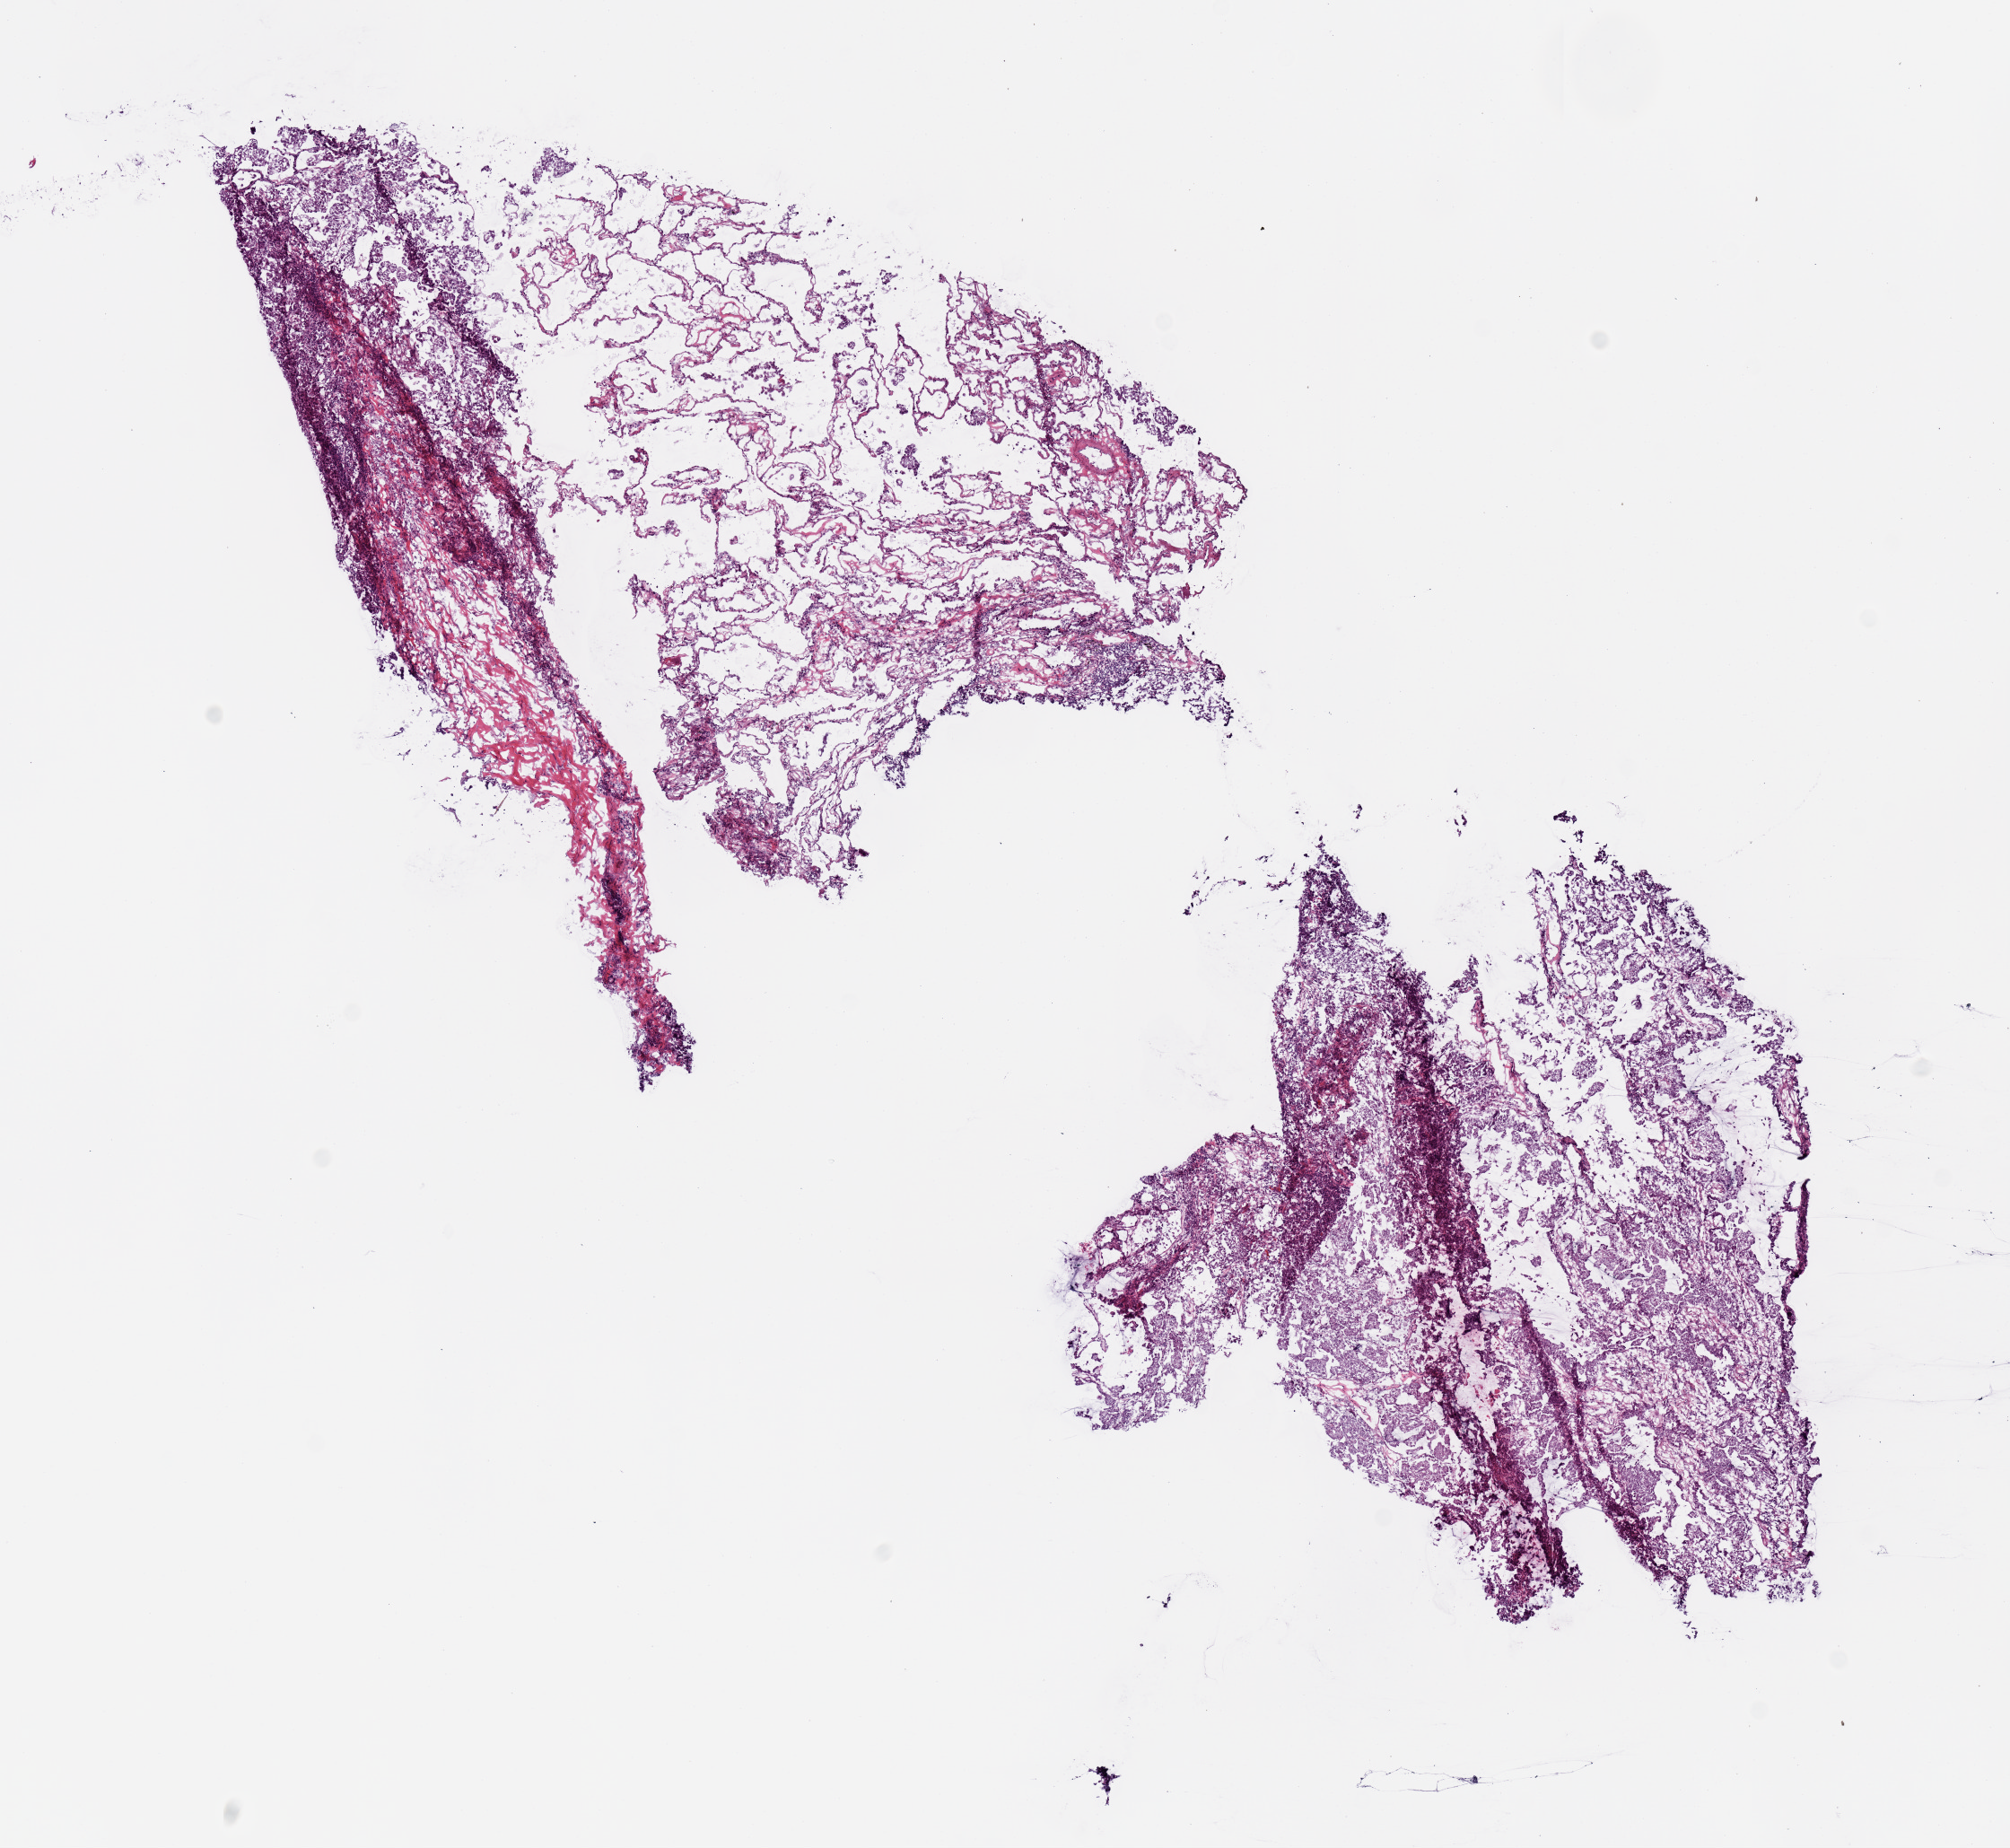
Whole-slide histology image, H&E-stained — shown as a low-resolution overview of the whole scanned area (about 8.9 x 8.1 mm, from a 20x scan). Frozen section from the bottom of the tissue portion. Primary tumour sample from the lung. Patient: female, age at initial diagnosis 67 years. Pathologist review of this section (percent, as recorded): tumour cells 50%, tumour nuclei 70%, normal cells 50%, stromal cells 0%, necrosis 0%. Inflammatory infiltration, as recorded: lymphocyte infiltration 15%, monocyte infiltration 3%, neutrophil infiltration 0%.
* AJCC pathologic stage: IIIA (6th edition)
* diagnosis: Papillary adenocarcinoma, NOS (upper lobe, lung)
* laterality: right